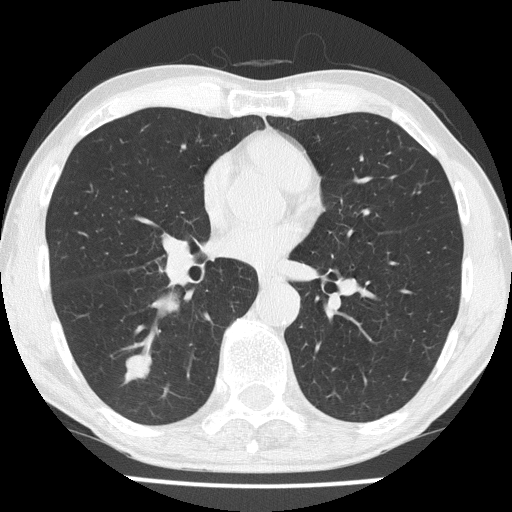
Chest CT (low-dose screening protocol), one axial image. Third annual screen. Lung window (W 1500 / L -600 HU). 2 mm slice thickness. Slice 104 of 186 in the series. Male, age 59 years at enrolment. Former smoker at enrolment.
• Expert reader's lesion annotation, bounding box [x1, y1, x2, y2] px = [113, 346, 159, 391].
• Reader record for this screening exam (exam-level; its link to the box is not recorded): non-calcified nodule or mass ≥4 mm, right lower lobe, 20 × 16 mm, smooth margins, soft tissue attenuation, pre-existing on the prior screen: no.
• Official screen result: positive, other.
• Later outcome: lung cancer diagnosed 25 days after this screen — small cell carcinoma, NOS, right lower lobe, stage IIA (AJCC 6th edition), 20 mm at pathology.